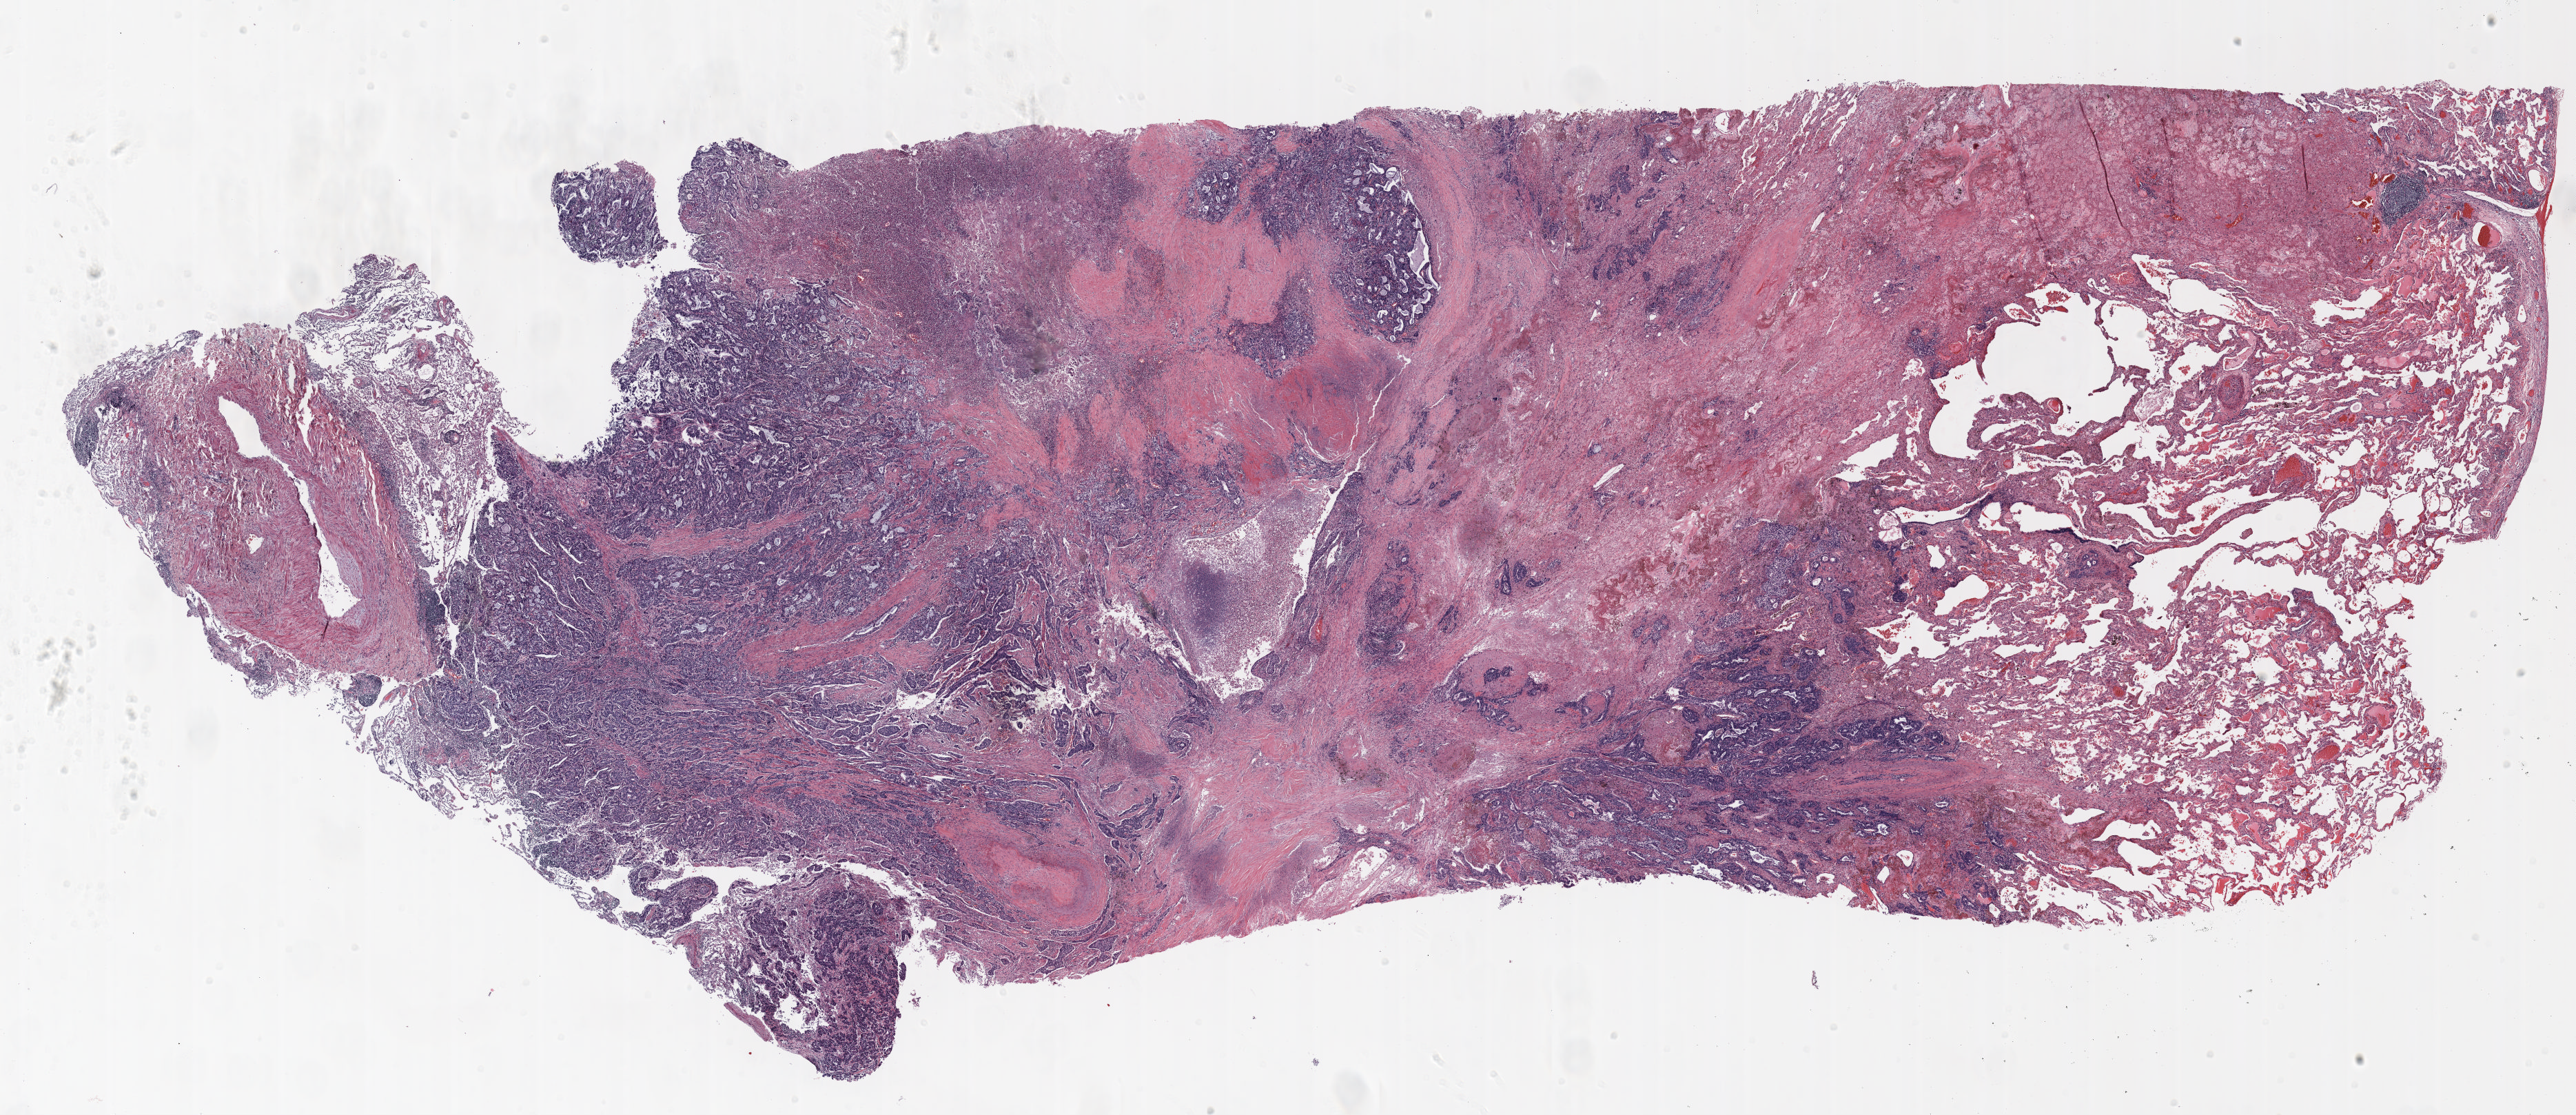
H&E whole-slide image, a low-resolution overview of the entire scanned area, about 30.0 x 13.0 mm. Formalin-fixed paraffin-embedded (FFPE) section. Lung tissue. Male patient, aged 64 at enrolment. Grade: moderately differentiated (G2).
Tumour size (pathology): 29 mm. Primary tumour location (clinical record): left upper lobe. Stage (AJCC 6th edition): IA. Participant's lung-cancer diagnosis: Adenocarcinoma, NOS.